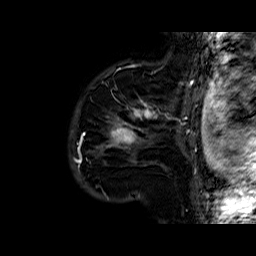
Breast MRI (dynamic contrast-enhanced), one sagittal slice. Slice 48 of 60 in the series (ordered by position). Dynamic contrast-enhanced series, time point 2 of 6 at this slice position (early post-contrast). 1.5 T. TE 6.4 ms, TR 32.8 ms. 4 mm slice thickness. 256 × 256 image matrix. Female patient. From the clinical record (not read from this slice): setting: breast cancer imaged before/during neoadjuvant chemotherapy; receptor status: HR-positive, HER2-negative.
Annotated regions visible in this slice (semi-automatic segmentation, software-assisted and operator-edited):
- analysis volume of interest (the breast-tissue region the enhancement analysis was run in; not a lesion): bounding box (x1, y1, x2, y2) in pixels: (87, 77, 163, 167)
- tumour enhancement mask (voxels above the 100 % enhancement threshold inside the analysis volume of interest): (107, 101, 157, 148)